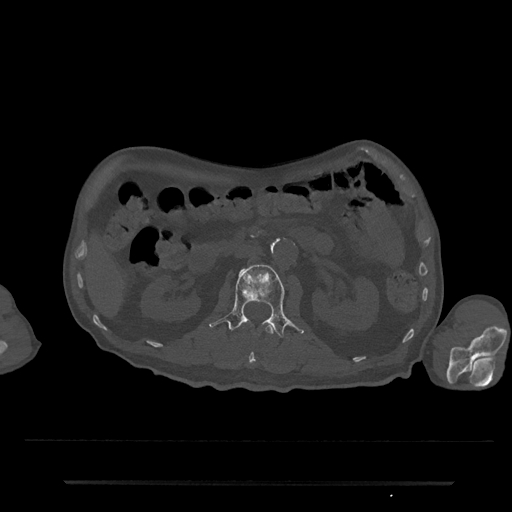
CT including the spine, one axial slice; 120 kVp; bone window (W 1800 / L 400 HU); 512 × 512 image matrix. Patient: male, 74 years. From the clinical record (not read from this slice): primary cancer: prostate.
Structures marked on this image (semi-automatically segmented with operator editing):
- L1 vertebra: bounding box [x1, y1, x2, y2] px = [242, 325, 274, 366]
- L2 vertebra: [209, 264, 304, 338]